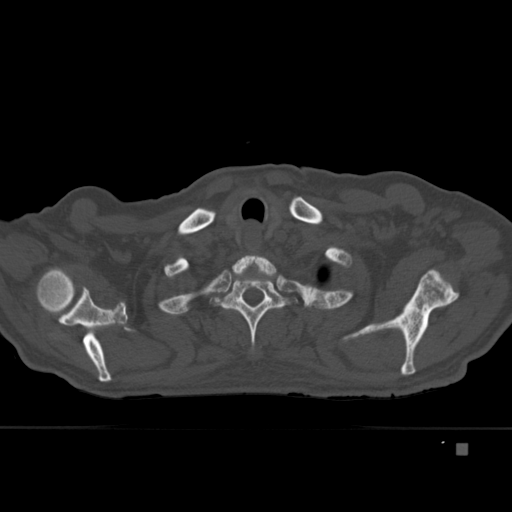
CT including the spine, one axial slice; position 349 of 451 along the scan axis; bone window (W 1800 / L 400 HU); 512 × 512 image matrix, field of view 378 × 378 mm. Patient: male, 75 years. Case-level facts recorded for this patient, not image findings: primary cancer: prostate.
Structures marked on this image (semi-automatically segmented with operator editing):
- T1 vertebra: bounding box (x1, y1, x2, y2) in pixels: (232, 255, 277, 284)
- T2 vertebra: (210, 257, 298, 353)